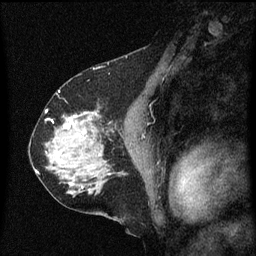
Breast MRI (dynamic contrast-enhanced), one sagittal slice; slice 35 of 60 in the series (ordered by position); dynamic contrast-enhanced series, image 2 of 3 at this slice position (ordered by acquisition); 1.5 T; TE 4.2 ms, TR 8 ms; 256 × 256 image matrix, field of view 200 × 200 mm. Patient: female, 58 years.
Structures marked on this image (semi-automatic segmentation, software-assisted and operator-edited):
- analysis volume of interest (the breast-tissue region the enhancement analysis was run in; not a lesion): bounding box <56,112,99,149> (left, top, right, bottom; pixels)
- tumour enhancement mask (voxels above the 70 % enhancement threshold inside the analysis volume of interest): <67,112,87,137>